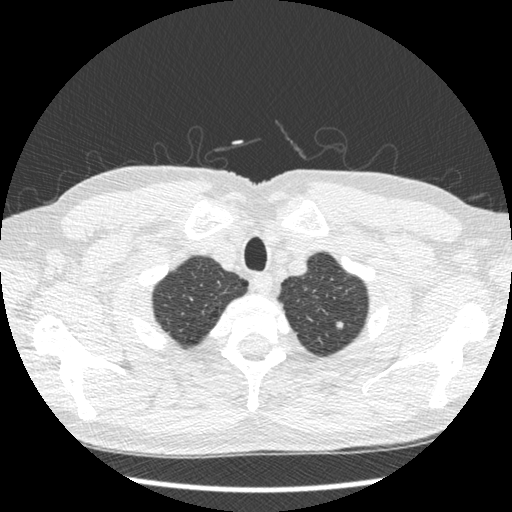
Low-dose screening chest CT, one axial slice. Position 408 of 439 along the scan axis. 120 kVp. Lung window (W 1500 / L -600 HU). 1.25 mm slice thickness. 512 × 512 image matrix, field of view 340 × 340 mm.
Annotated regions visible in this slice (outlined manually by an expert reader):
- lesion 1 (nodule, upper lobe of left lung): bounding box (x1, y1, x2, y2) in pixels: (336, 321, 344, 329)